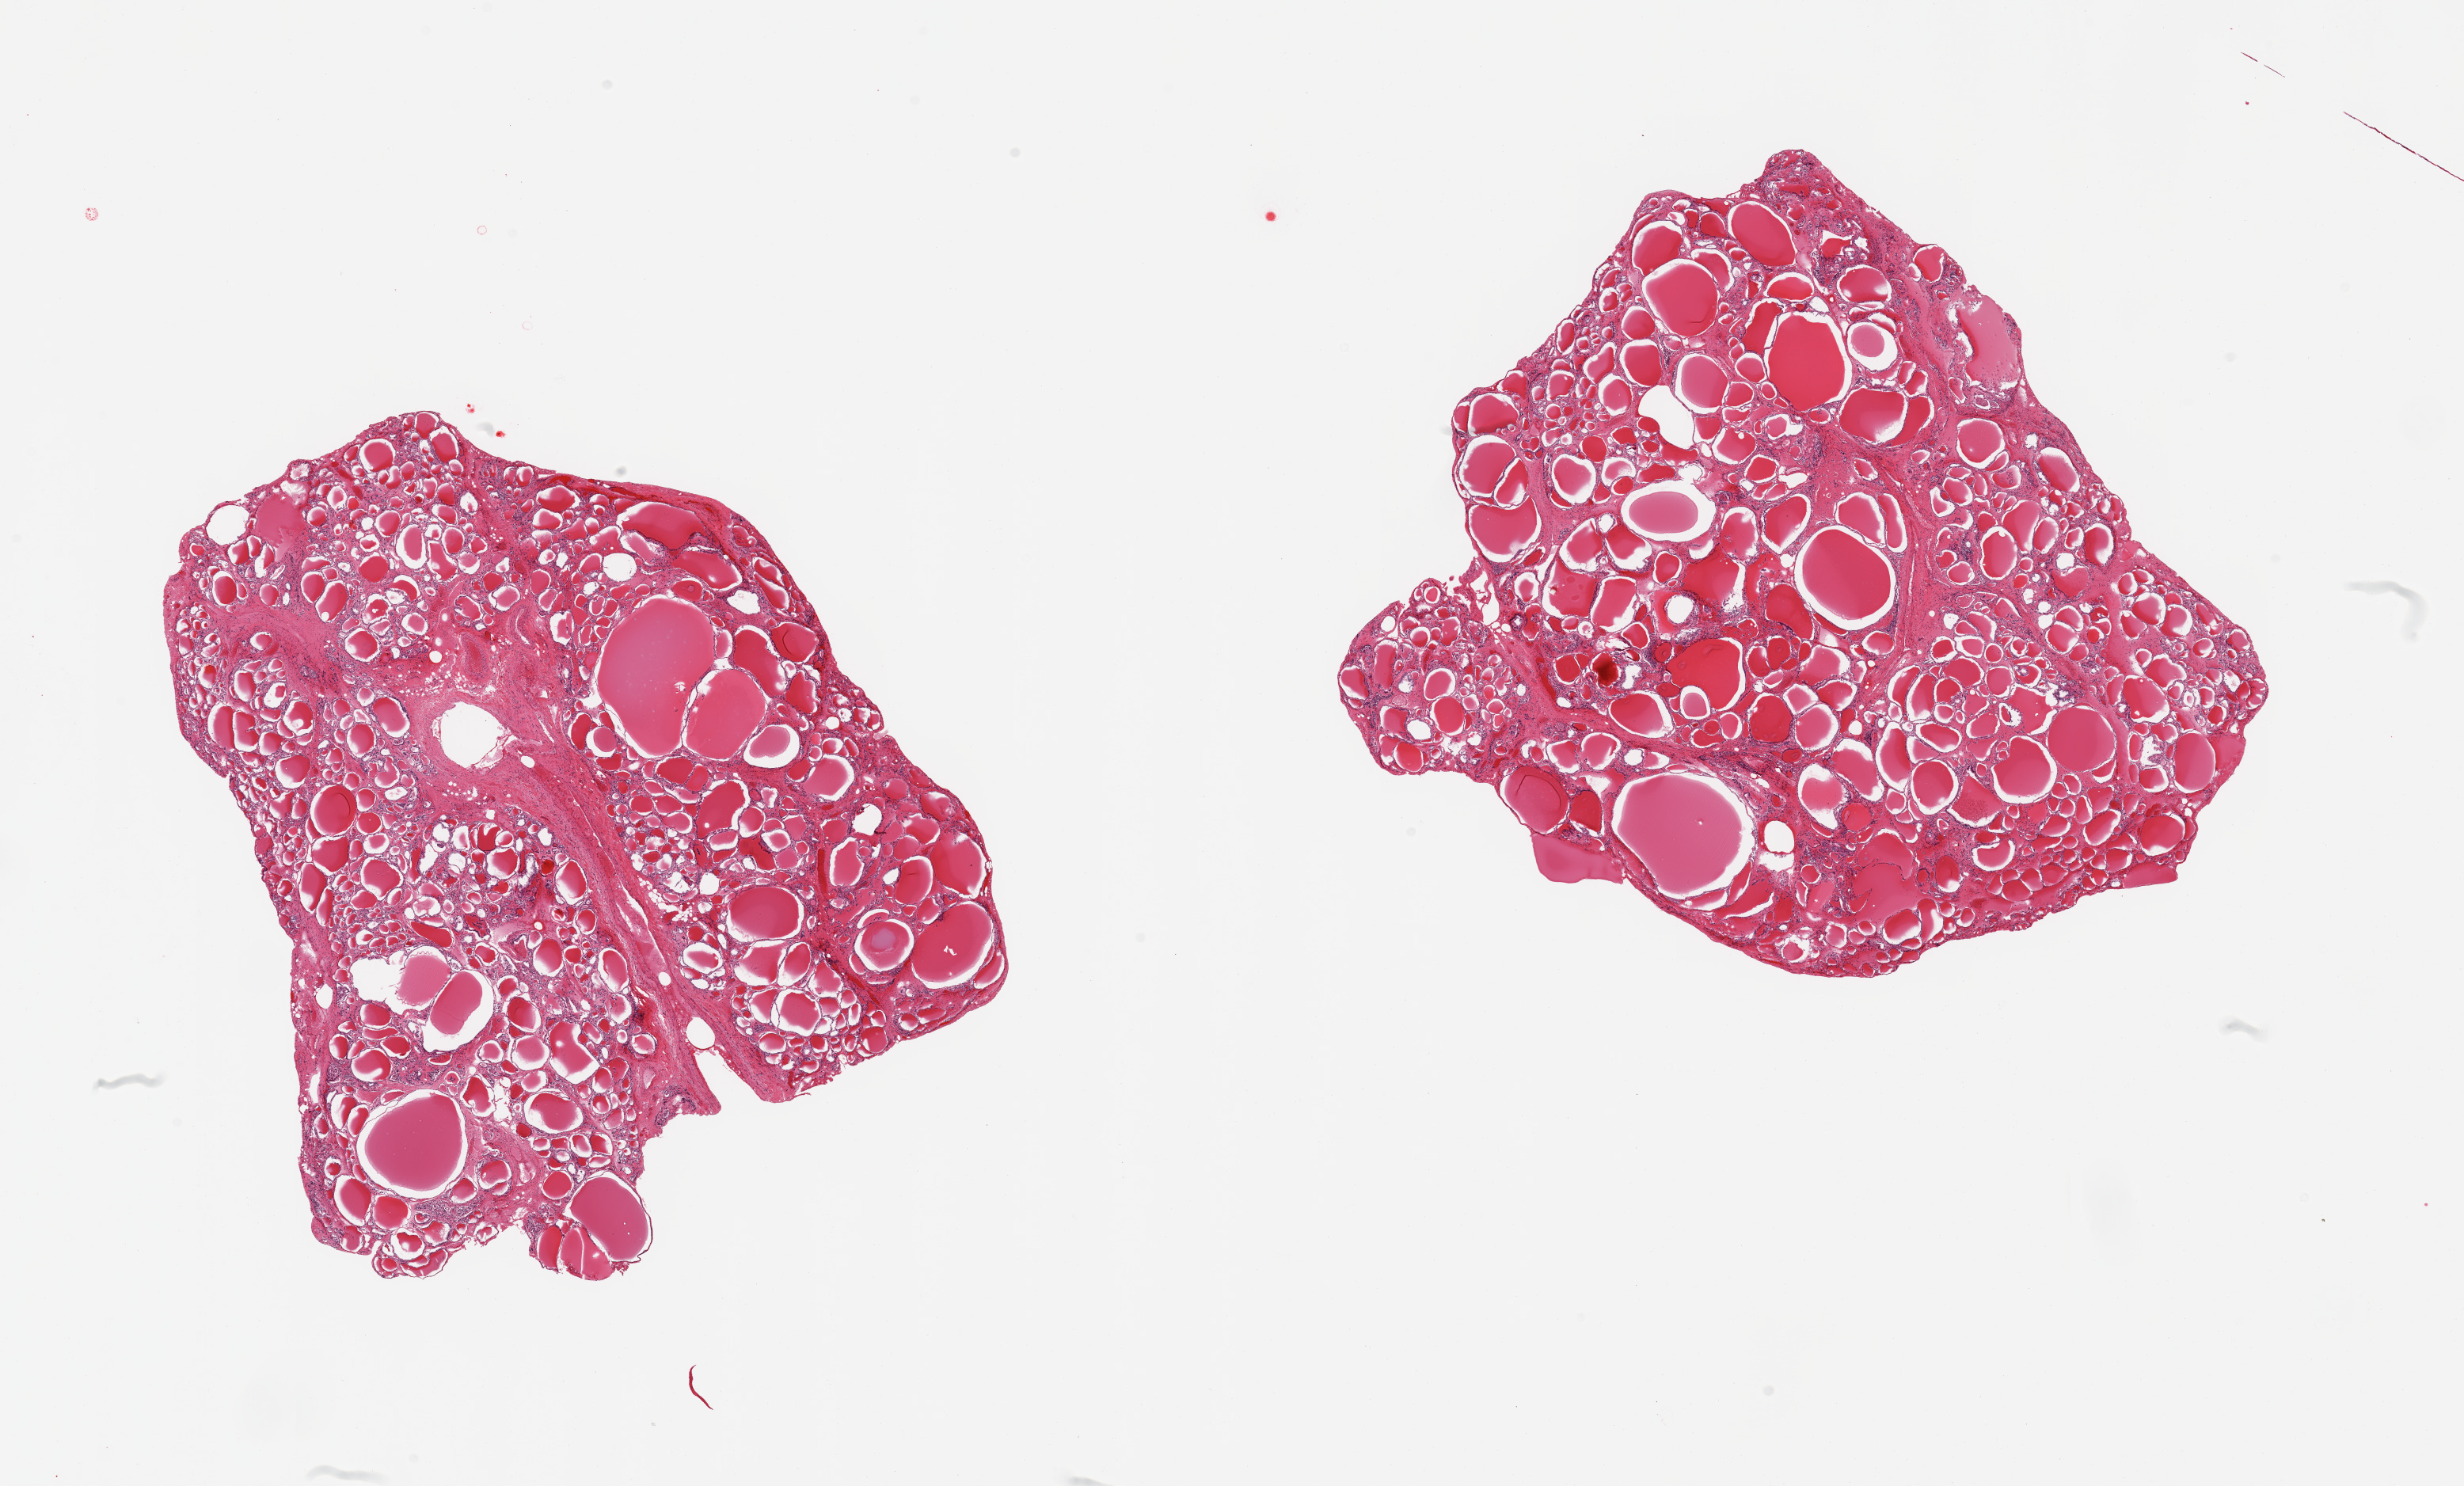
Digitized hematoxylin and eosin (H&E)-stained section — a low-resolution overview of the entire scanned area, about 24.6 x 14.8 mm, PAXgene-fixed, paraffin-embedded tissue, section of thyroid (target tissue), donor tissue sample. Male donor.
* review note (as recorded): 2 pieces; nodular